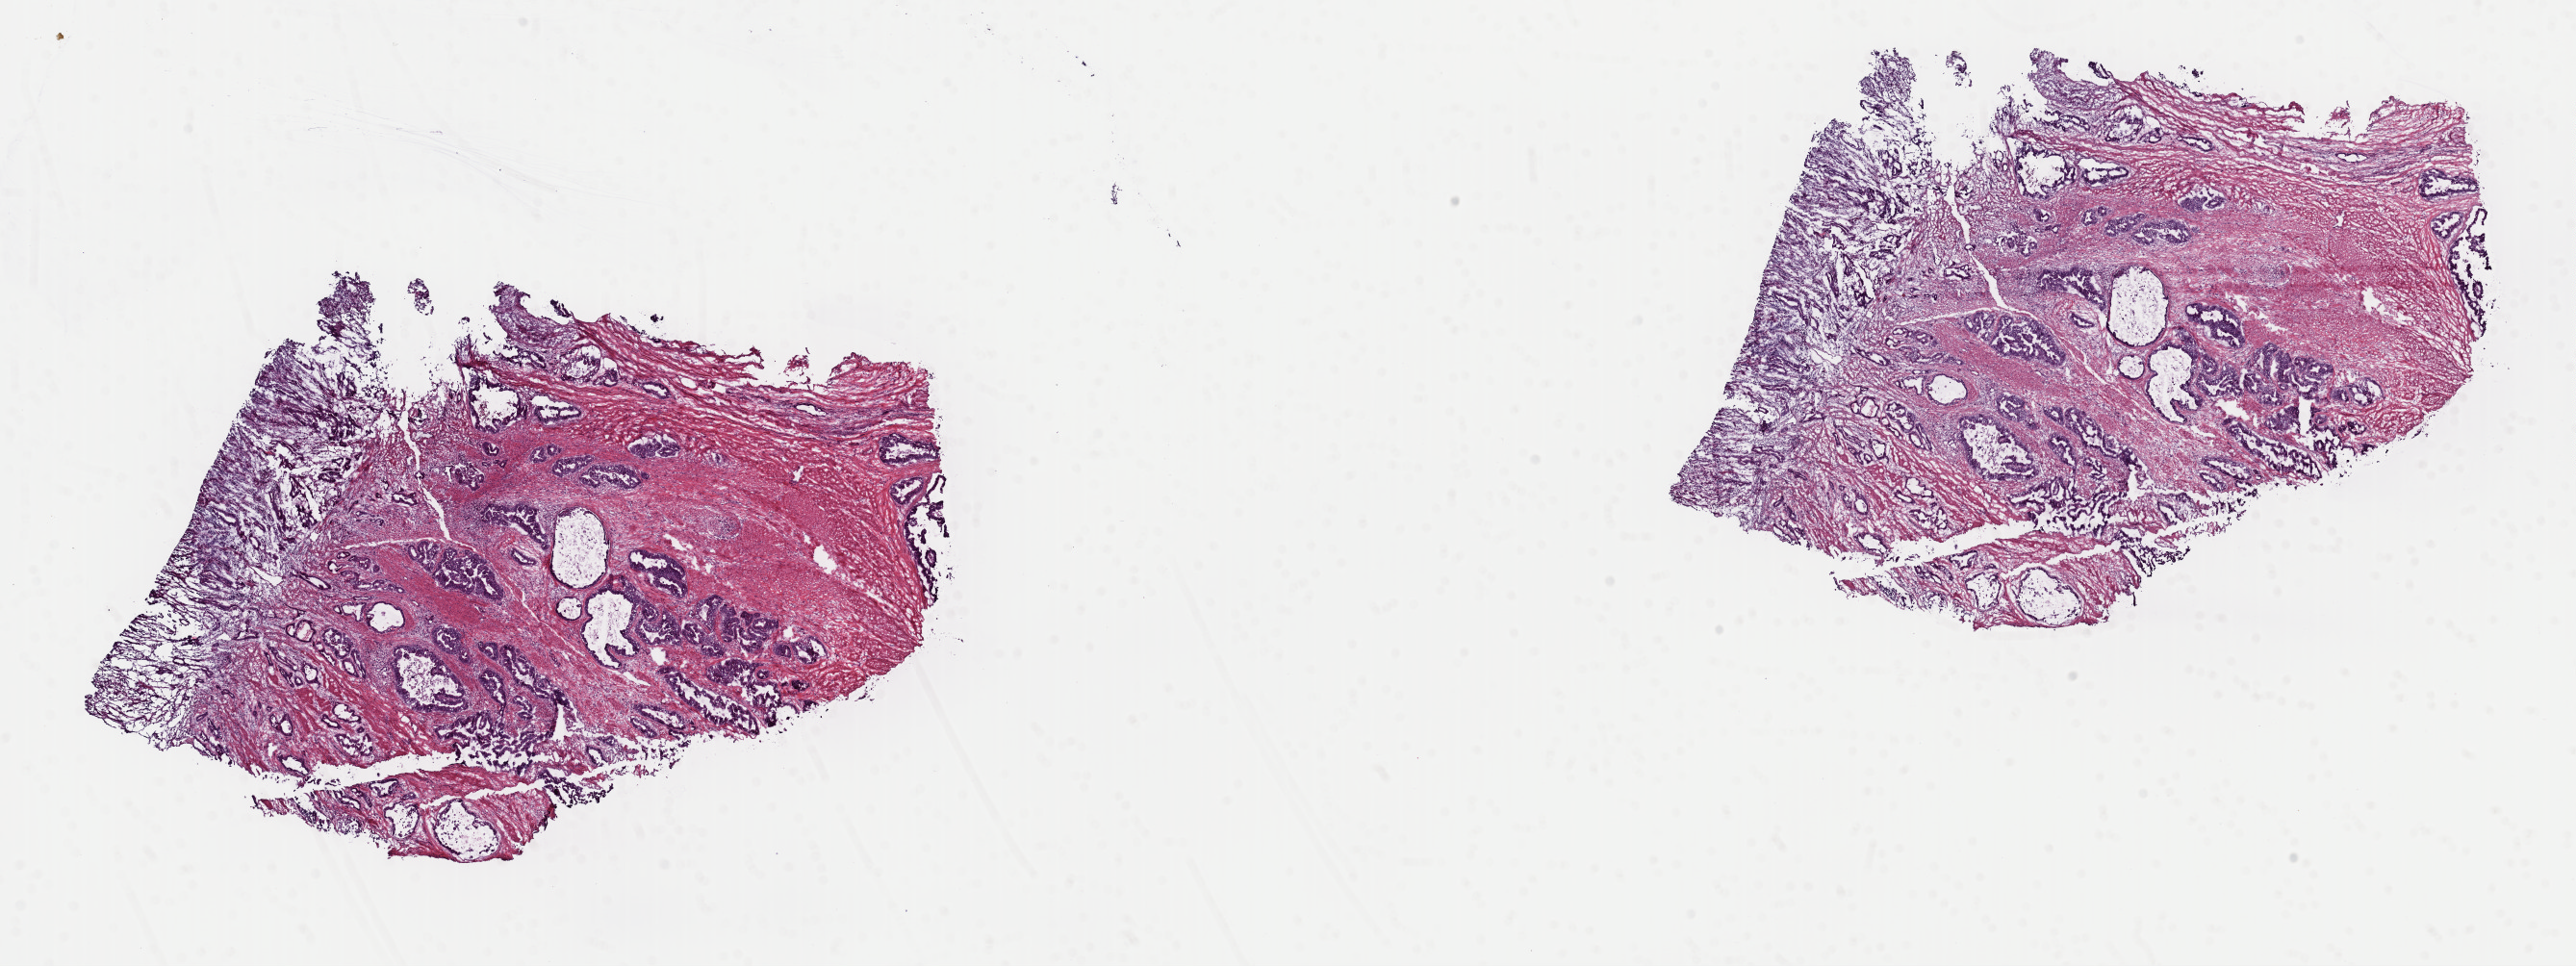
Digitized H&E tissue section (whole slide) — whole scanned area (about 21.1 x 7.9 mm, slide scanned at 40x) shown as a low-resolution overview. Frozen section. Primary tumour sample from the stomach. Patient: male, age at initial diagnosis 74 years. Histologic grade: G1 (well differentiated). Pathologist review of this section (percent, as recorded): tumour cells 35%, tumour nuclei 70%, normal cells 0%, stromal cells 61%, necrosis 4%. Inflammatory infiltration, as recorded: lymphocyte infiltration 4%, monocyte infiltration 2%, neutrophil infiltration 4%.
• AJCC pathologic stage: IIB (7th edition)
• TNM: T4a NX M0
• histologic diagnosis: Adenocarcinoma, intestinal type (fundus of stomach)